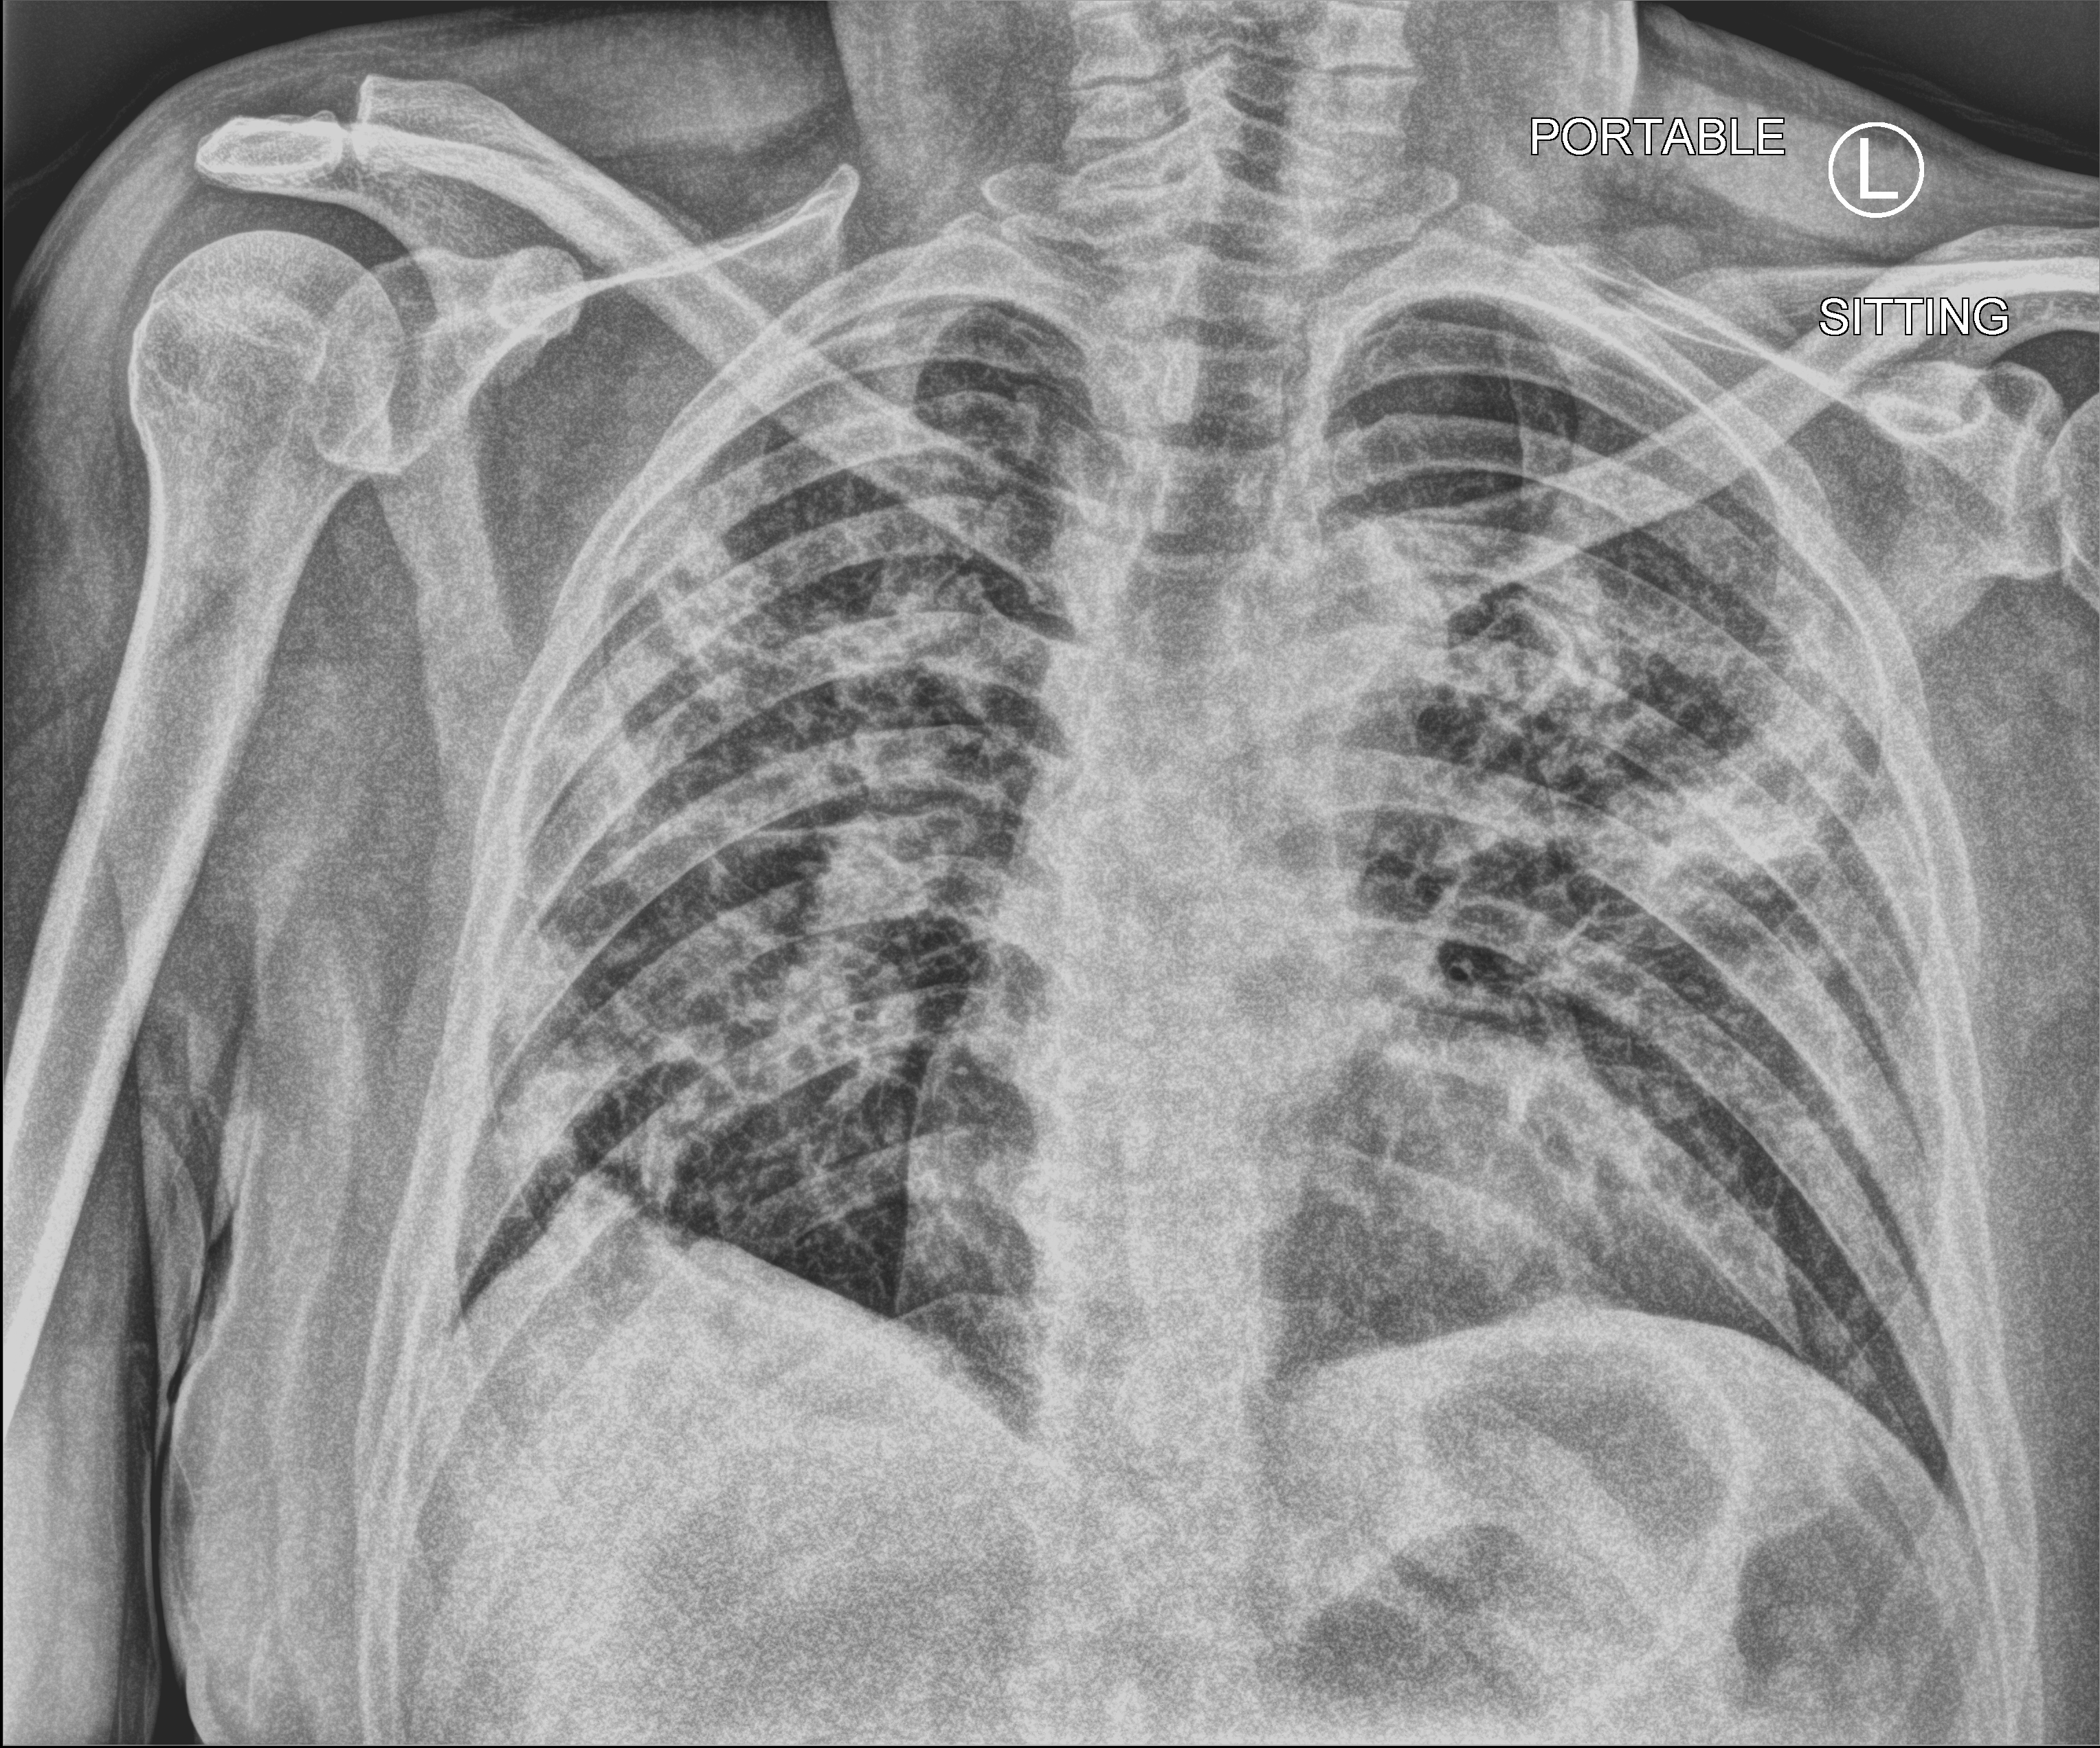
Portable chest radiograph, anteroposterior (AP) projection. Male patient hospitalised with COVID-19, age 18–59 years.
Hospital-stay facts (about this admission, not read from this image; timing relative to this image not recorded): admitted to intensive care during this hospital stay: no.